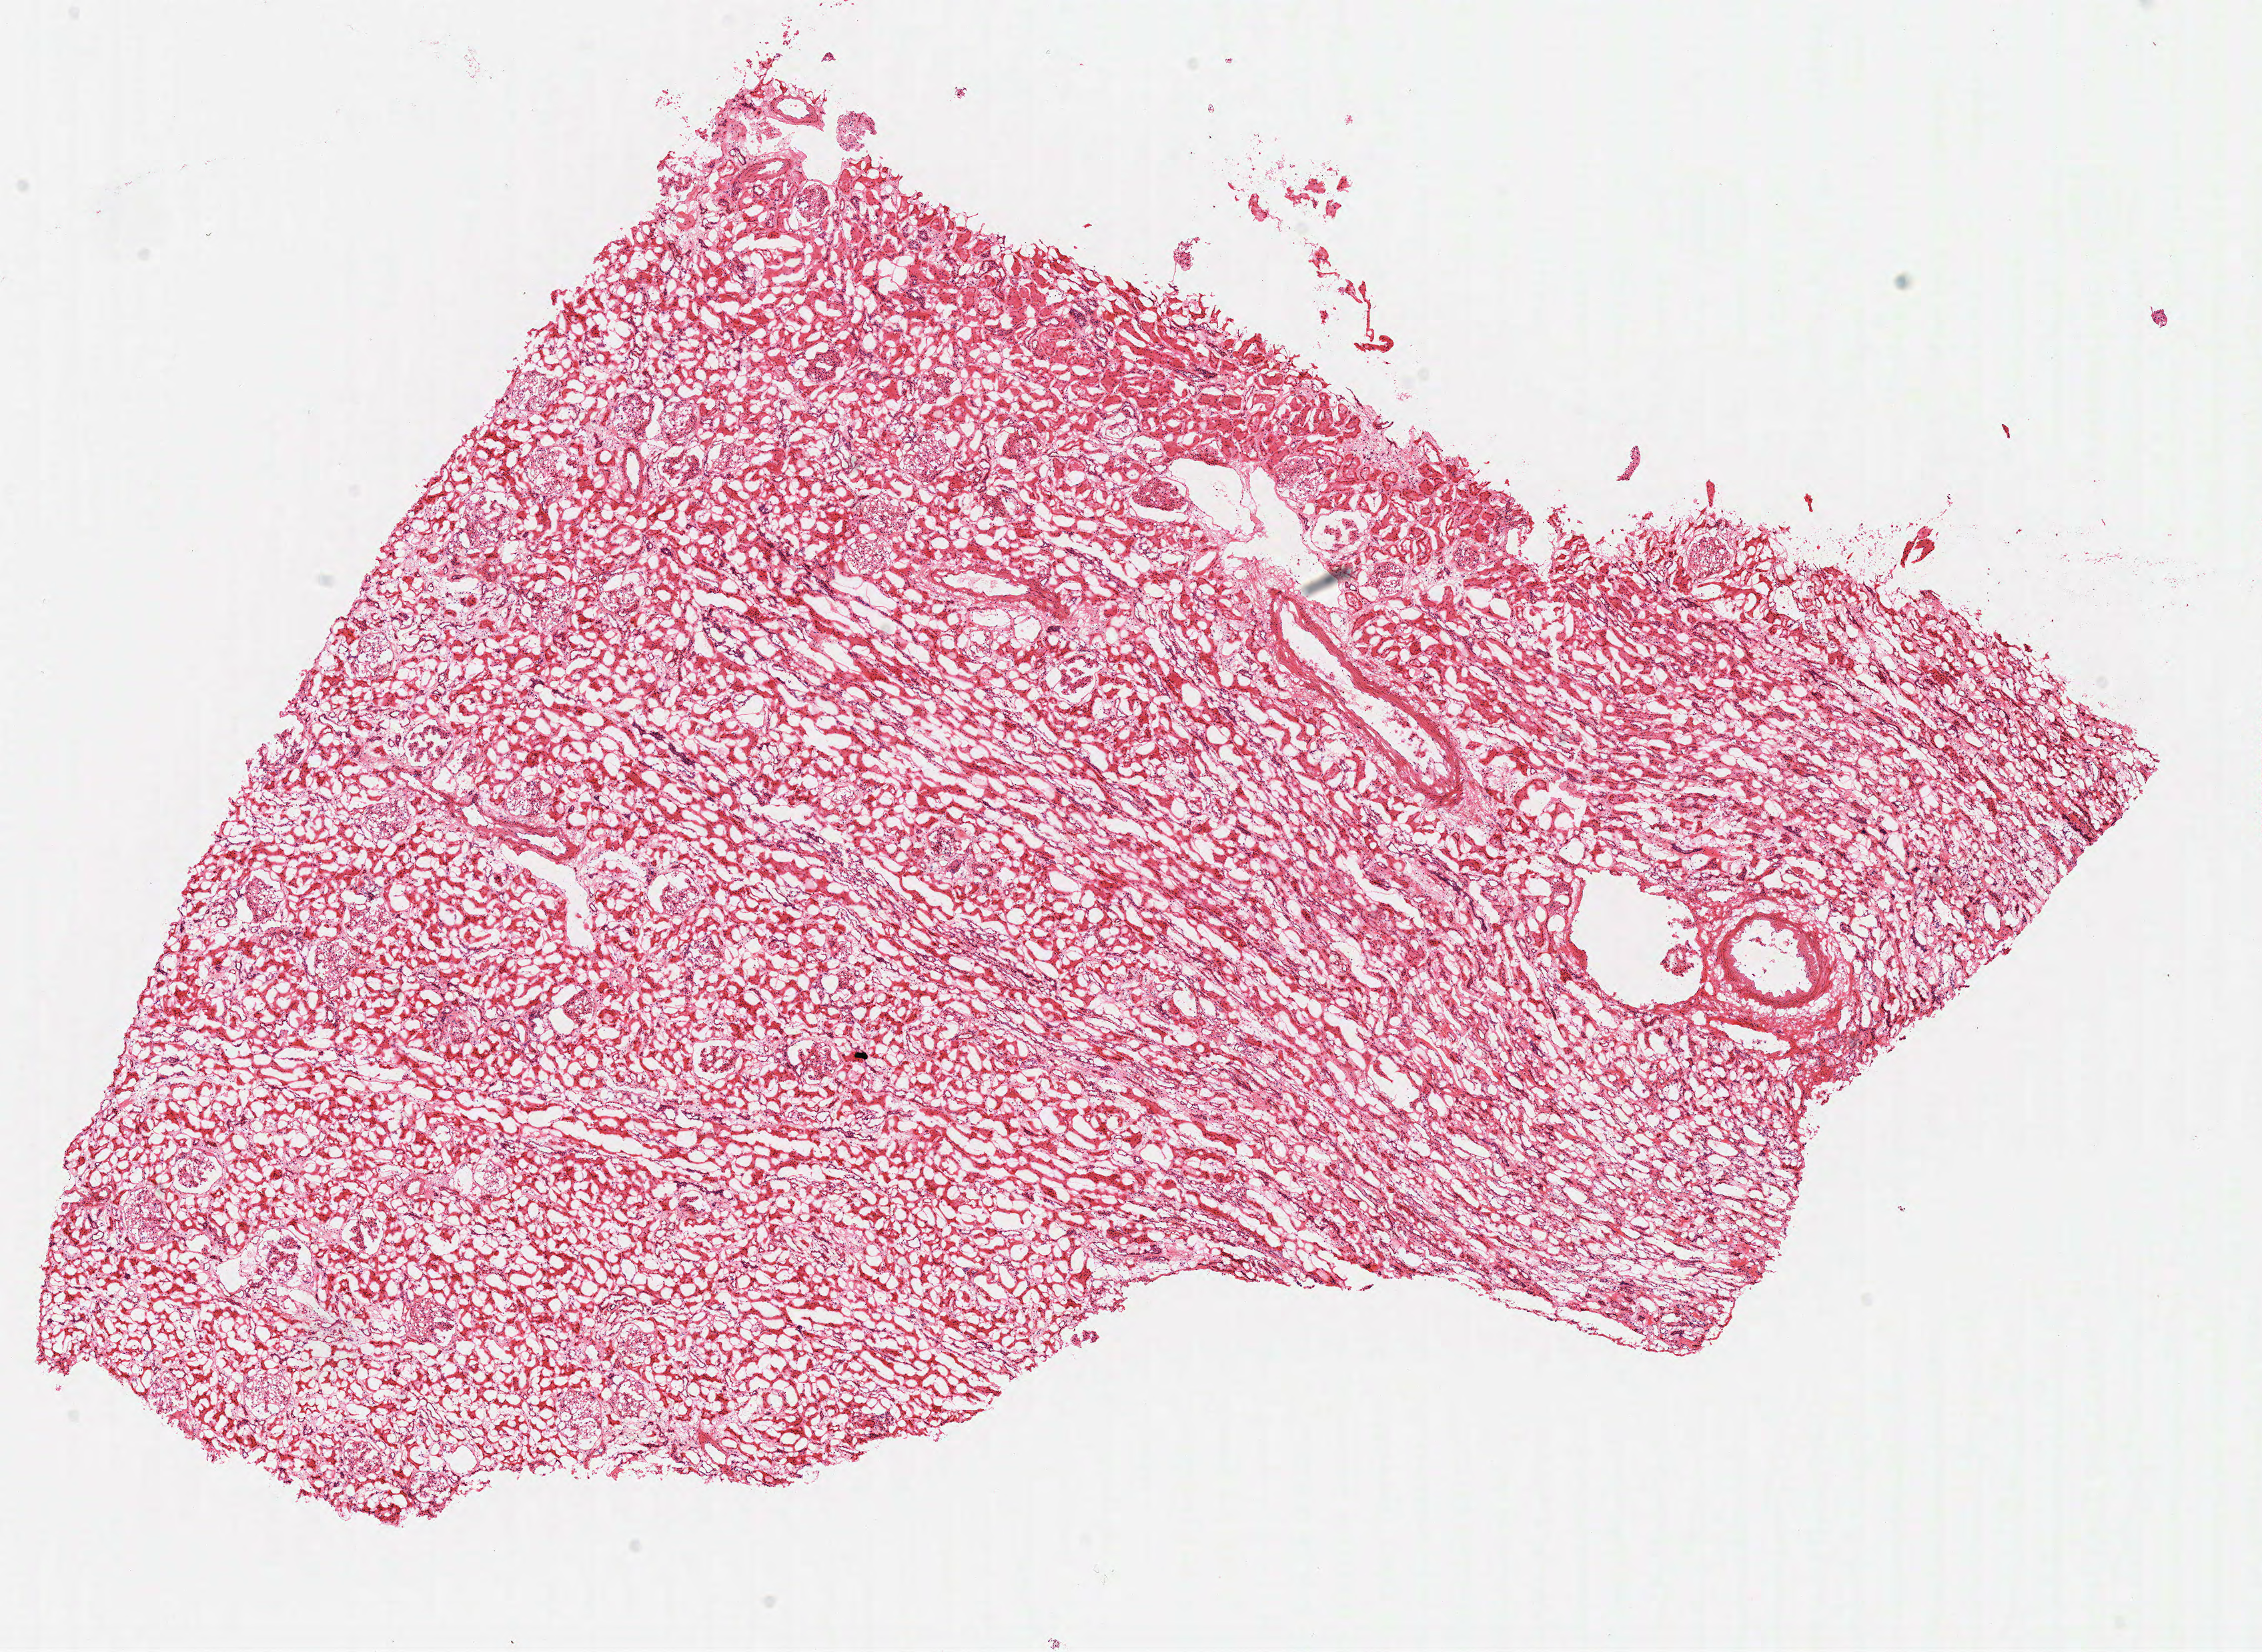
Hematoxylin and eosin (H&E) stained whole-slide image, low-resolution overview of the scanned area, about 13.4 x 9.8 mm (acquisition: 40x scan); frozen section from the top of the tissue portion; sample: solid tissue normal (non-tumour tissue), kidney. Male patient; age at initial diagnosis 58 years.
This section: solid tissue normal sample (biorepository sample class). Patient diagnosis: Clear cell adenocarcinoma, NOS.